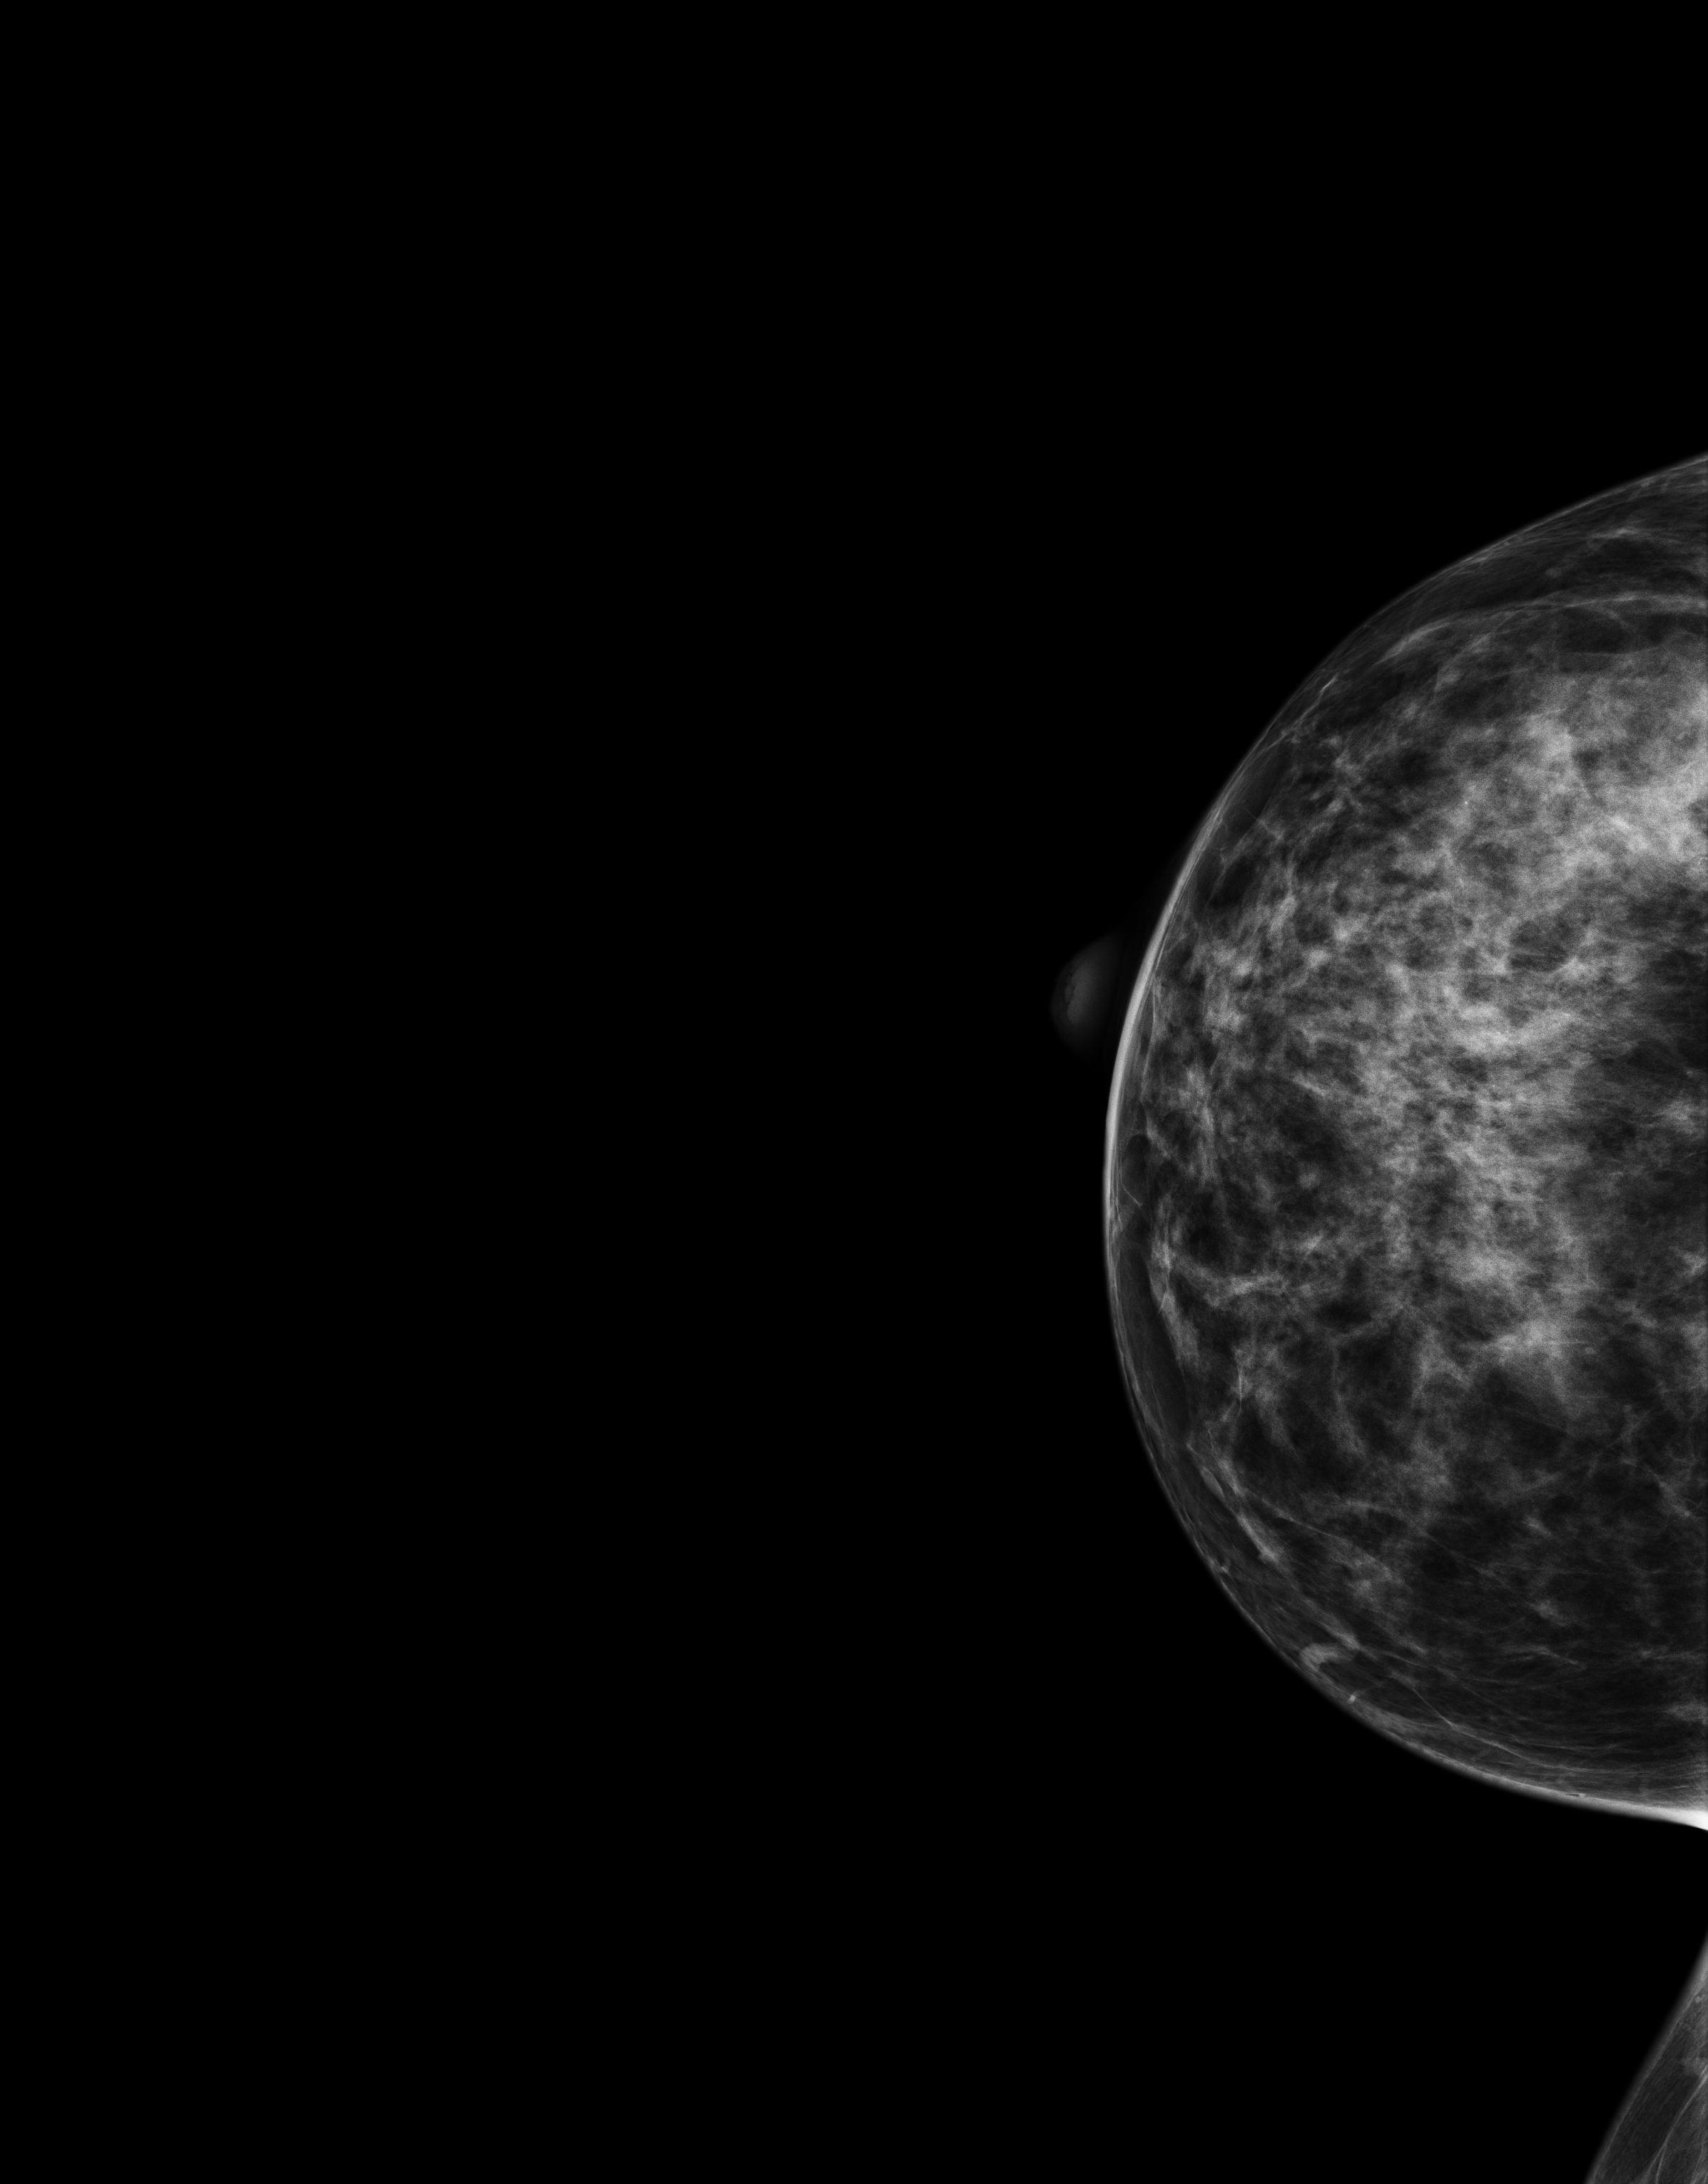
Screening examination, system: Senographe Essential ADS_56.21.3. Patient: female, 43 years.
Image type: full-field digital mammogram. Breast: right. Projection: craniocaudal (CC) view.